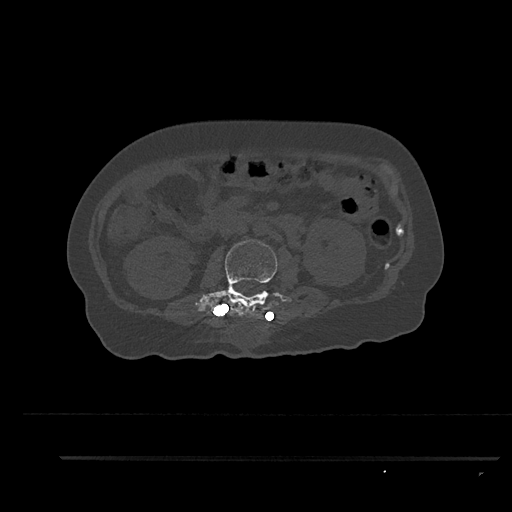
CT including the spine, one axial slice; position 149 of 797 along the scan axis; reconstruction kernel Br40s/3; bone window (W 1800 / L 400 HU); 0.5 mm slice thickness; 512 × 512 image matrix, field of view 408 × 408 mm. Female patient, age 44 years. From the clinical record (not read from this slice): primary cancer: renal; vertebrae with lytic lesions (as recorded): L1.
Outlined on this slice (semi-automatically segmented with operator editing):
- L2 vertebra: bounding box <195,239,280,320> (left, top, right, bottom; pixels)